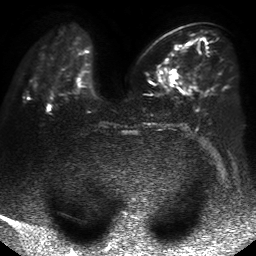
Breast MRI, one axial slice; slice 21 of 50 in the series (ordered by position); diffusion-weighted series; image 2 of 4 stored at this slice position (different b-values; order by instance number); 1.5 T; 4 mm slice thickness; 256 × 256 image matrix, field of view 360 × 360 mm. Female patient.
Annotated regions visible in this slice (outlined manually by an expert reader):
- tumour on diffusion-weighted imaging: box from (x=168, y=45) to (x=180, y=80) px